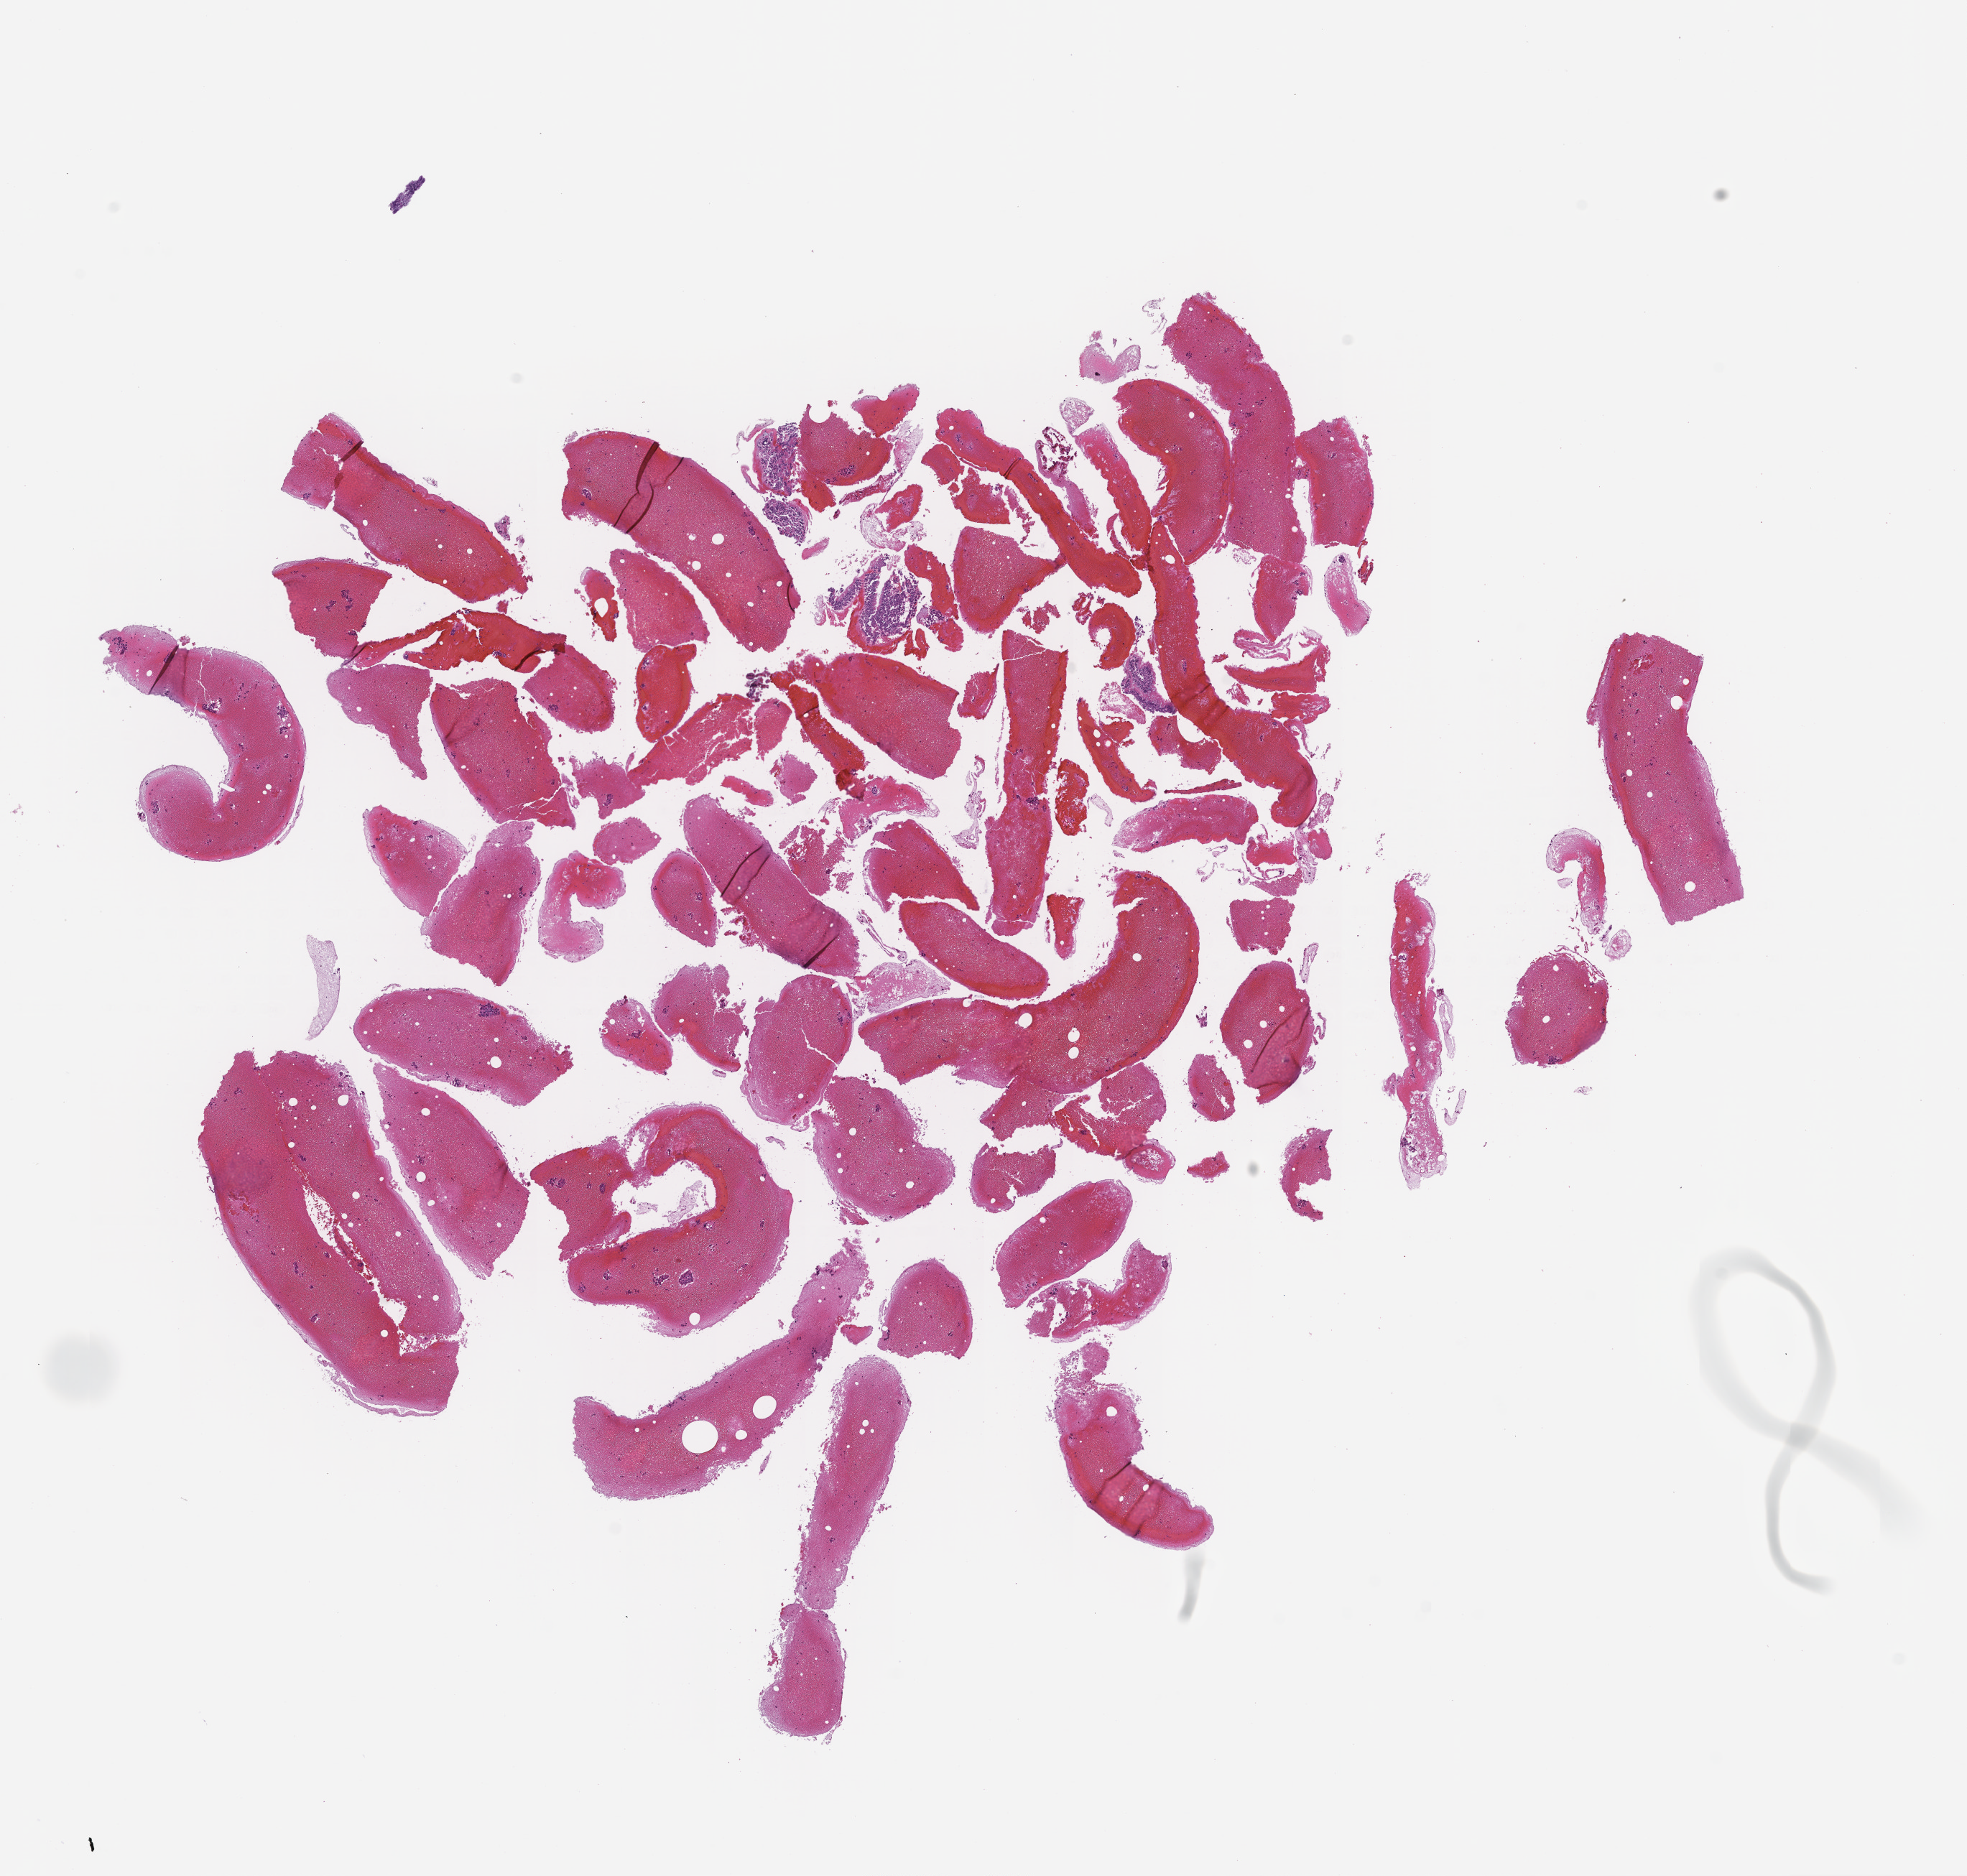
Hematoxylin and eosin (H&E) whole-slide image, a low-resolution overview of the entire scanned area, about 11.1 x 10.5 mm, formalin-fixed, paraffin-embedded (FFPE) tissue. Patient: female.
* this section: metastasis (sampled organ not recorded)
* patient diagnosis (primary): Invasive Breast Carcinoma